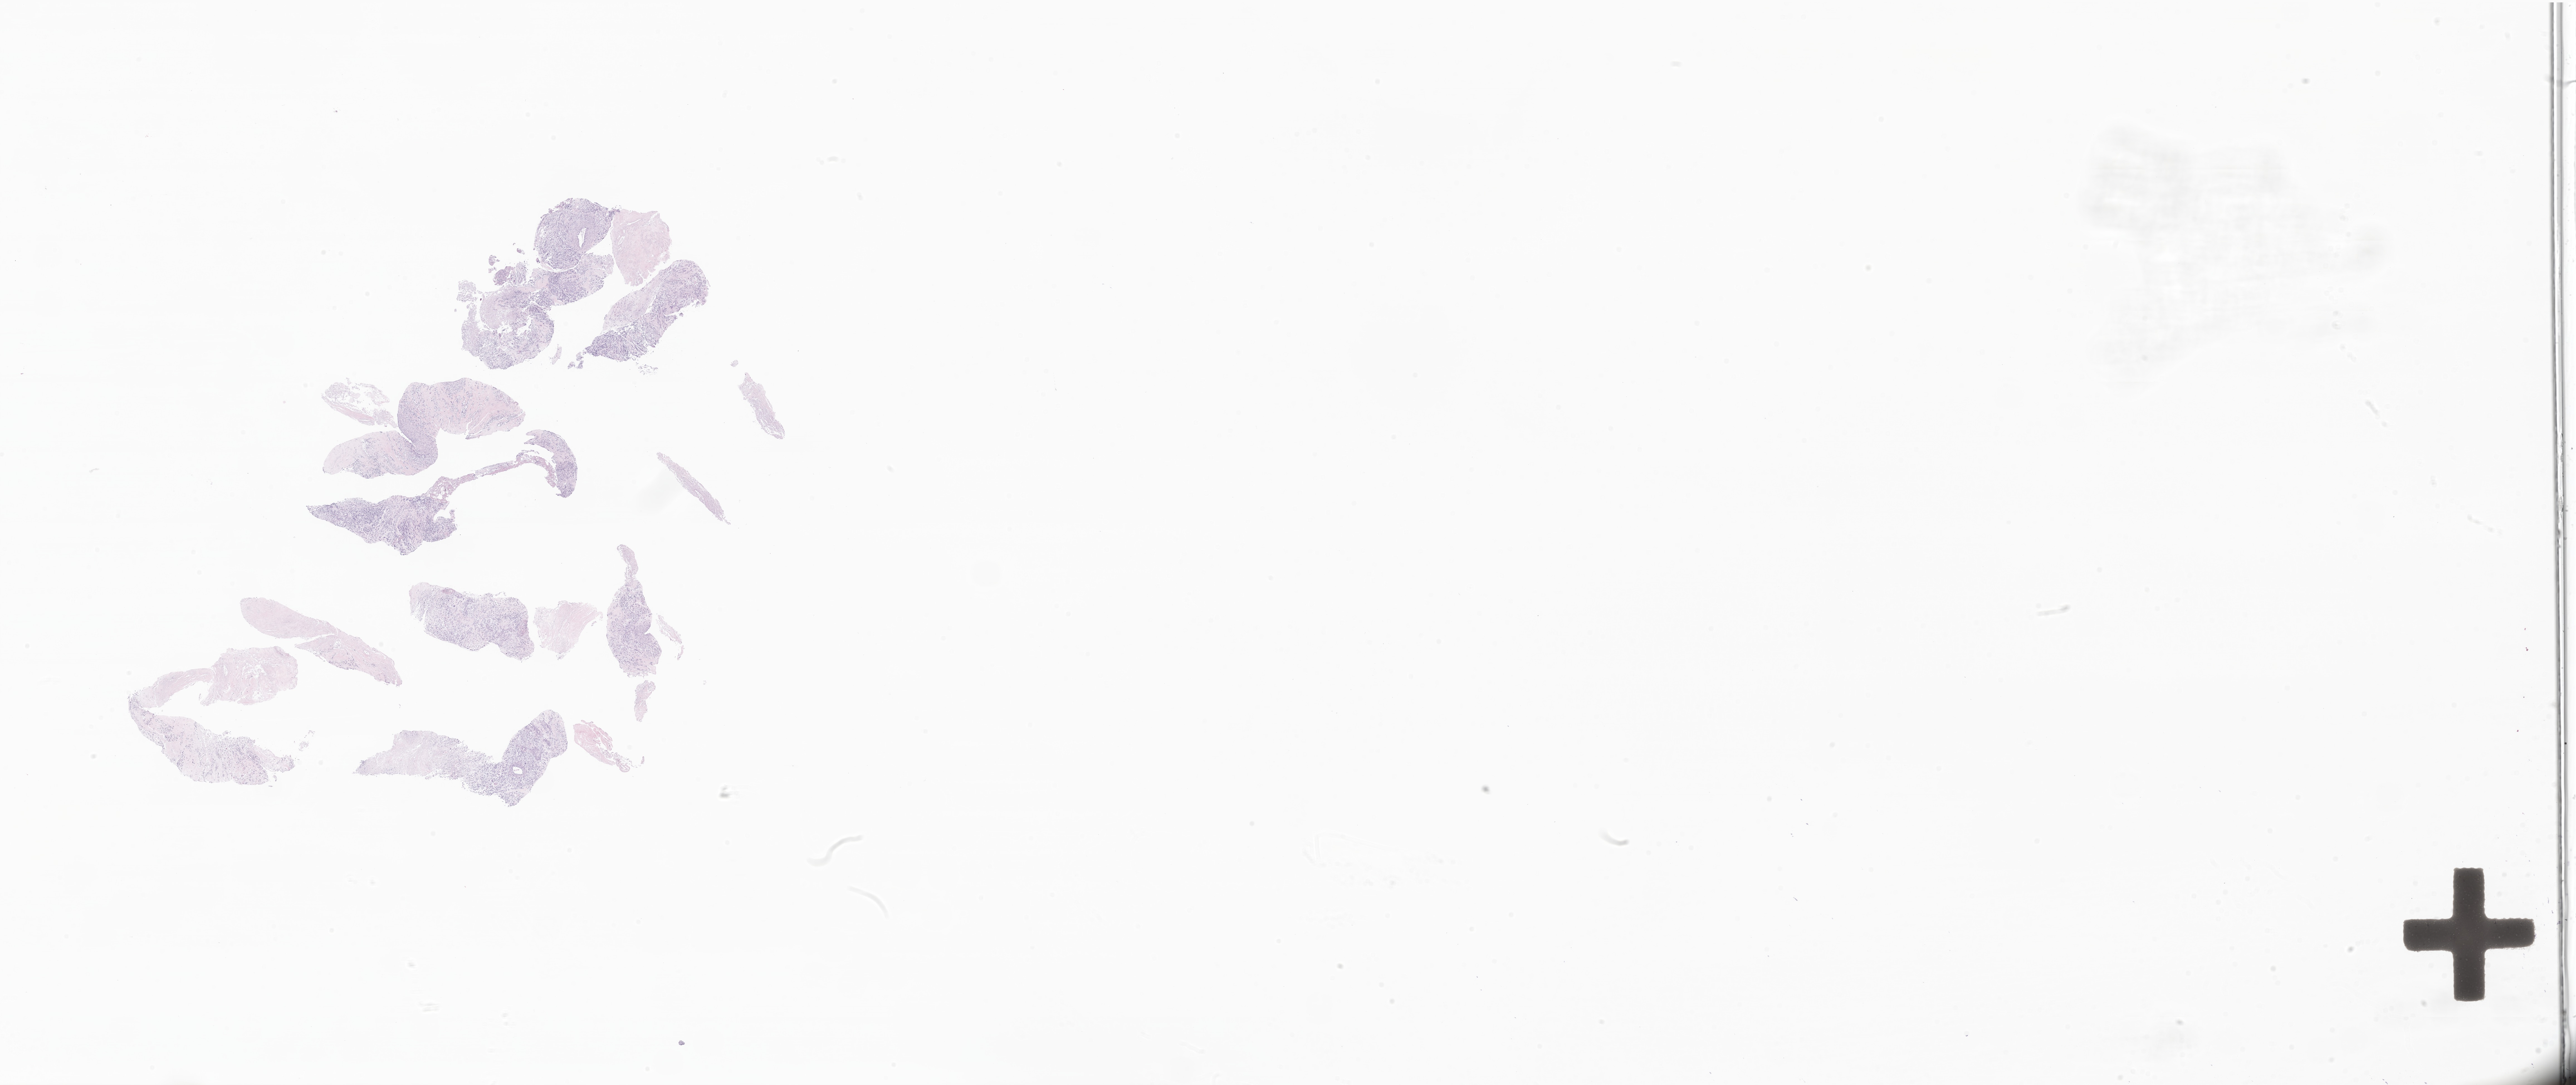
Digitized H&E-stained section of tumor tissue from the anterior mediastinum, a low-resolution overview of the entire scanned area, about 39.0 x 16.4 mm, formalin-fixed paraffin-embedded section. Patient male; age 224 months (18 years 8 months).
Diagnosis: Rhabdomyosarcoma, NOS.